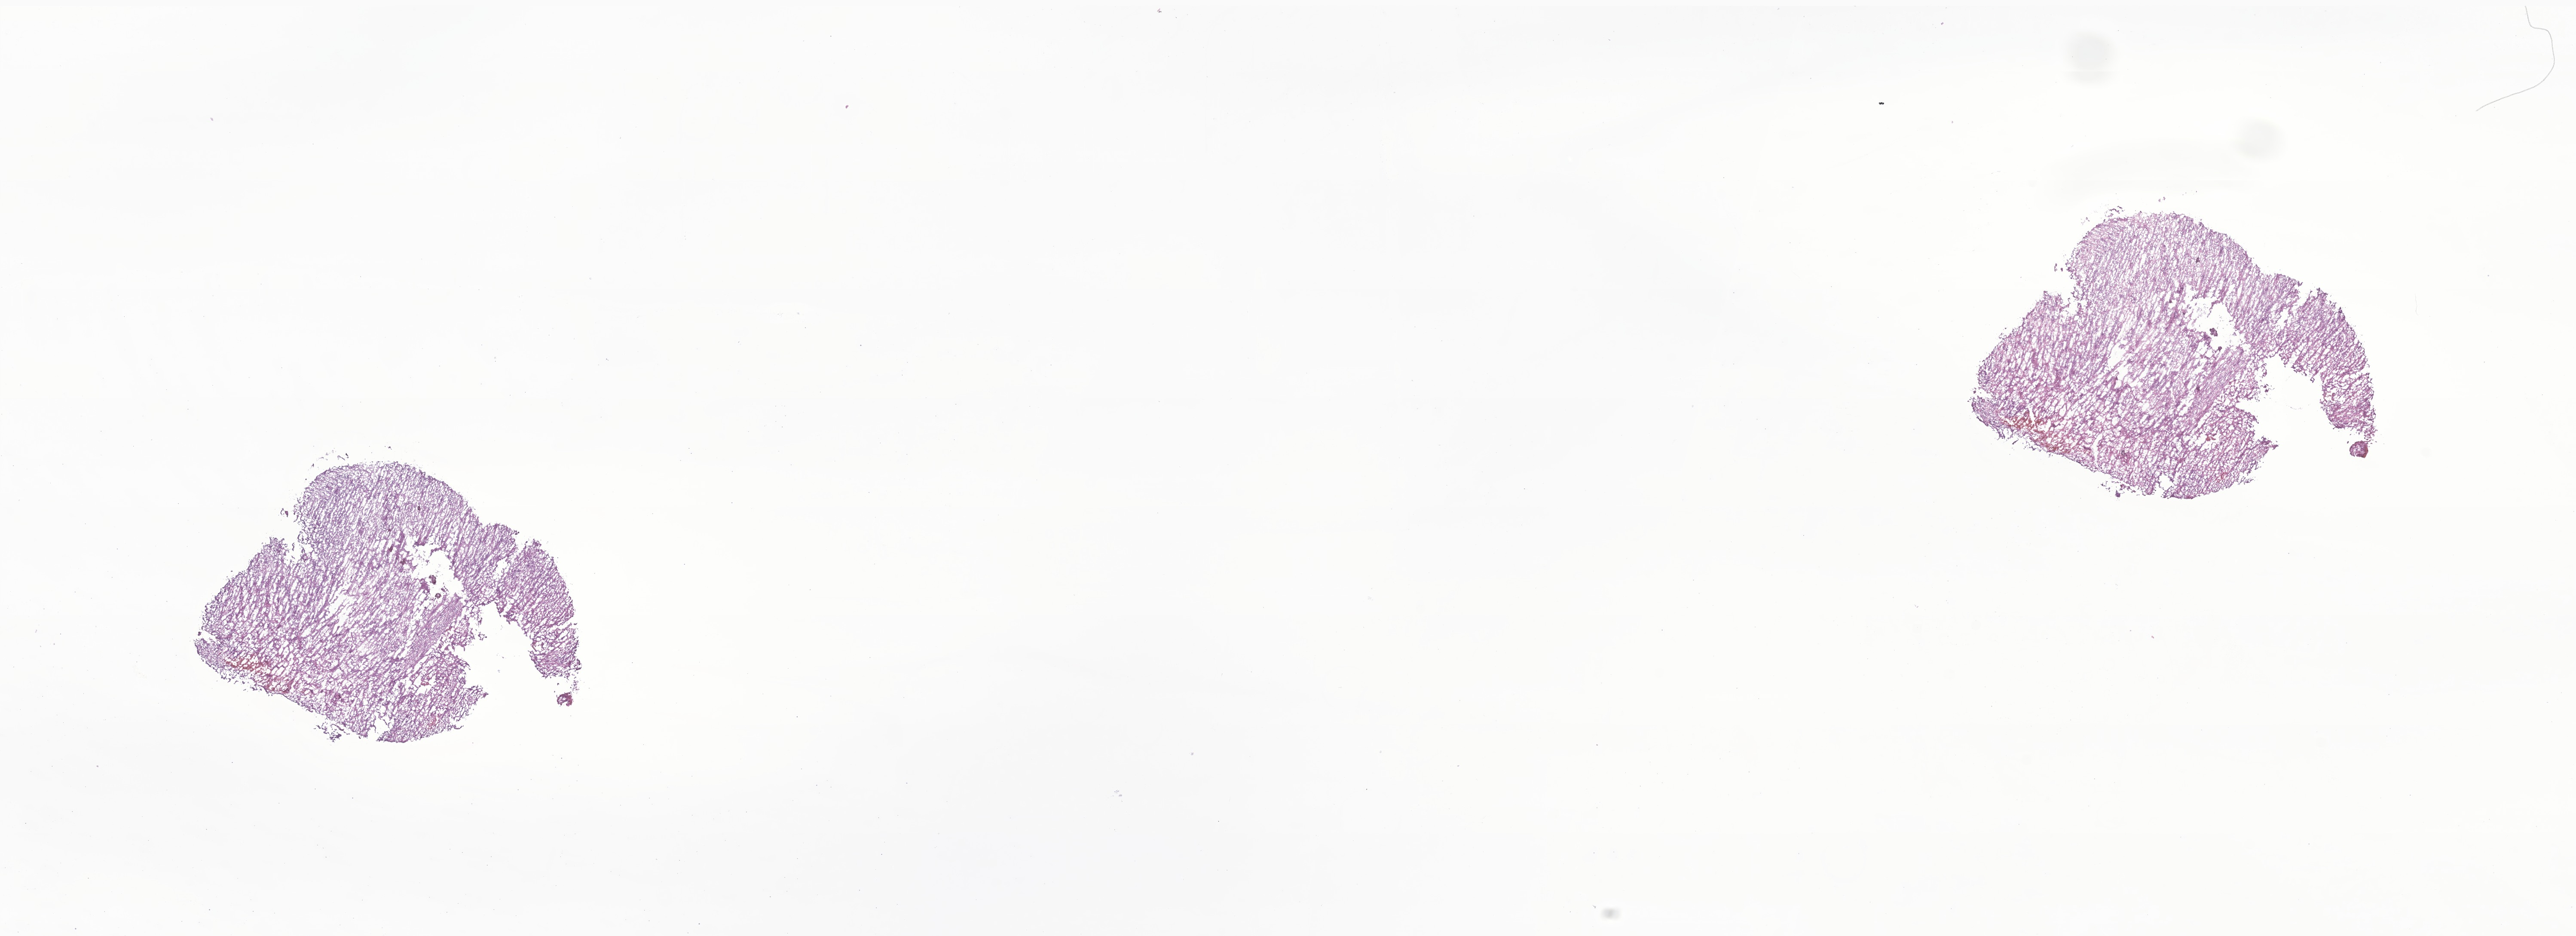
Whole-slide image, hematoxylin and eosin (H&E) stain of tumor tissue from the brain — shown as a low-resolution overview of the whole scanned area (about 25.3 x 9.2 mm), cryosection (OCT / tissue freezing medium). Patient: female, age 78 months.
Diagnosis (ICD-O-3 morphology term): Ependymoma, NOS.